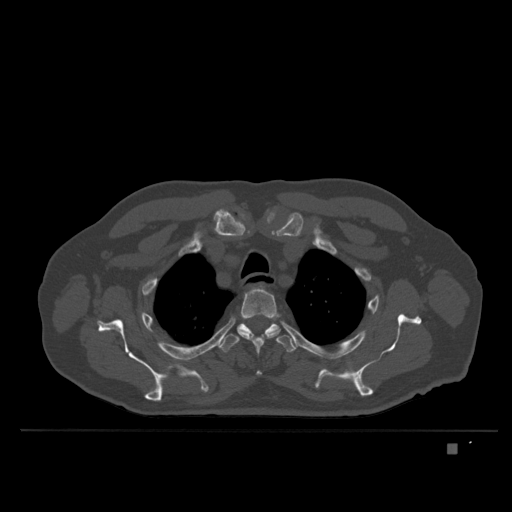
CT including the spine, one axial slice; position 296 of 435 along the scan axis; bone window (W 1800 / L 400 HU); 1.5 mm slice thickness; 512 × 512 image matrix, field of view 434 × 434 mm. Patient: male, 73 years. Case-level facts recorded for this patient, not image findings: primary cancer: skin.
Outlined on this slice (semi-automatically segmented with operator editing):
- T3 vertebra: bounding box (x1, y1, x2, y2) in pixels: (237, 288, 279, 376)
- T4 vertebra: (219, 322, 297, 353)